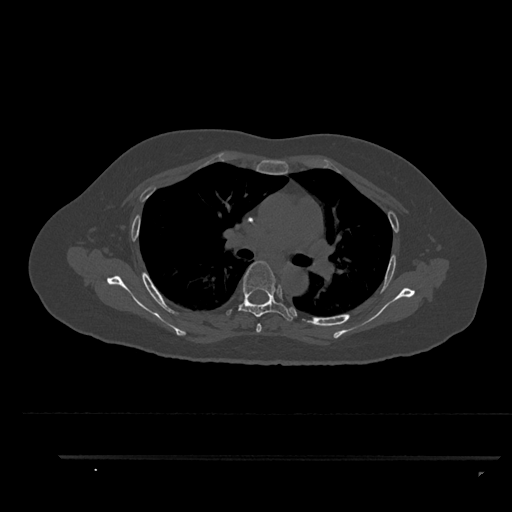
CT including the spine, one axial slice. Position 606 of 797 along the scan axis. Bone window (W 1800 / L 400 HU). 512 × 512 image matrix, field of view 408 × 408 mm. Female patient, age 44 years. Case-level facts recorded for this patient, not image findings: primary cancer: renal.
Annotated regions visible in this slice (semi-automatic segmentation, software-assisted and operator-edited):
- T4 vertebra: bounding box (x1, y1, x2, y2) in pixels: (256, 323, 262, 333)
- T5 vertebra: (226, 261, 293, 321)